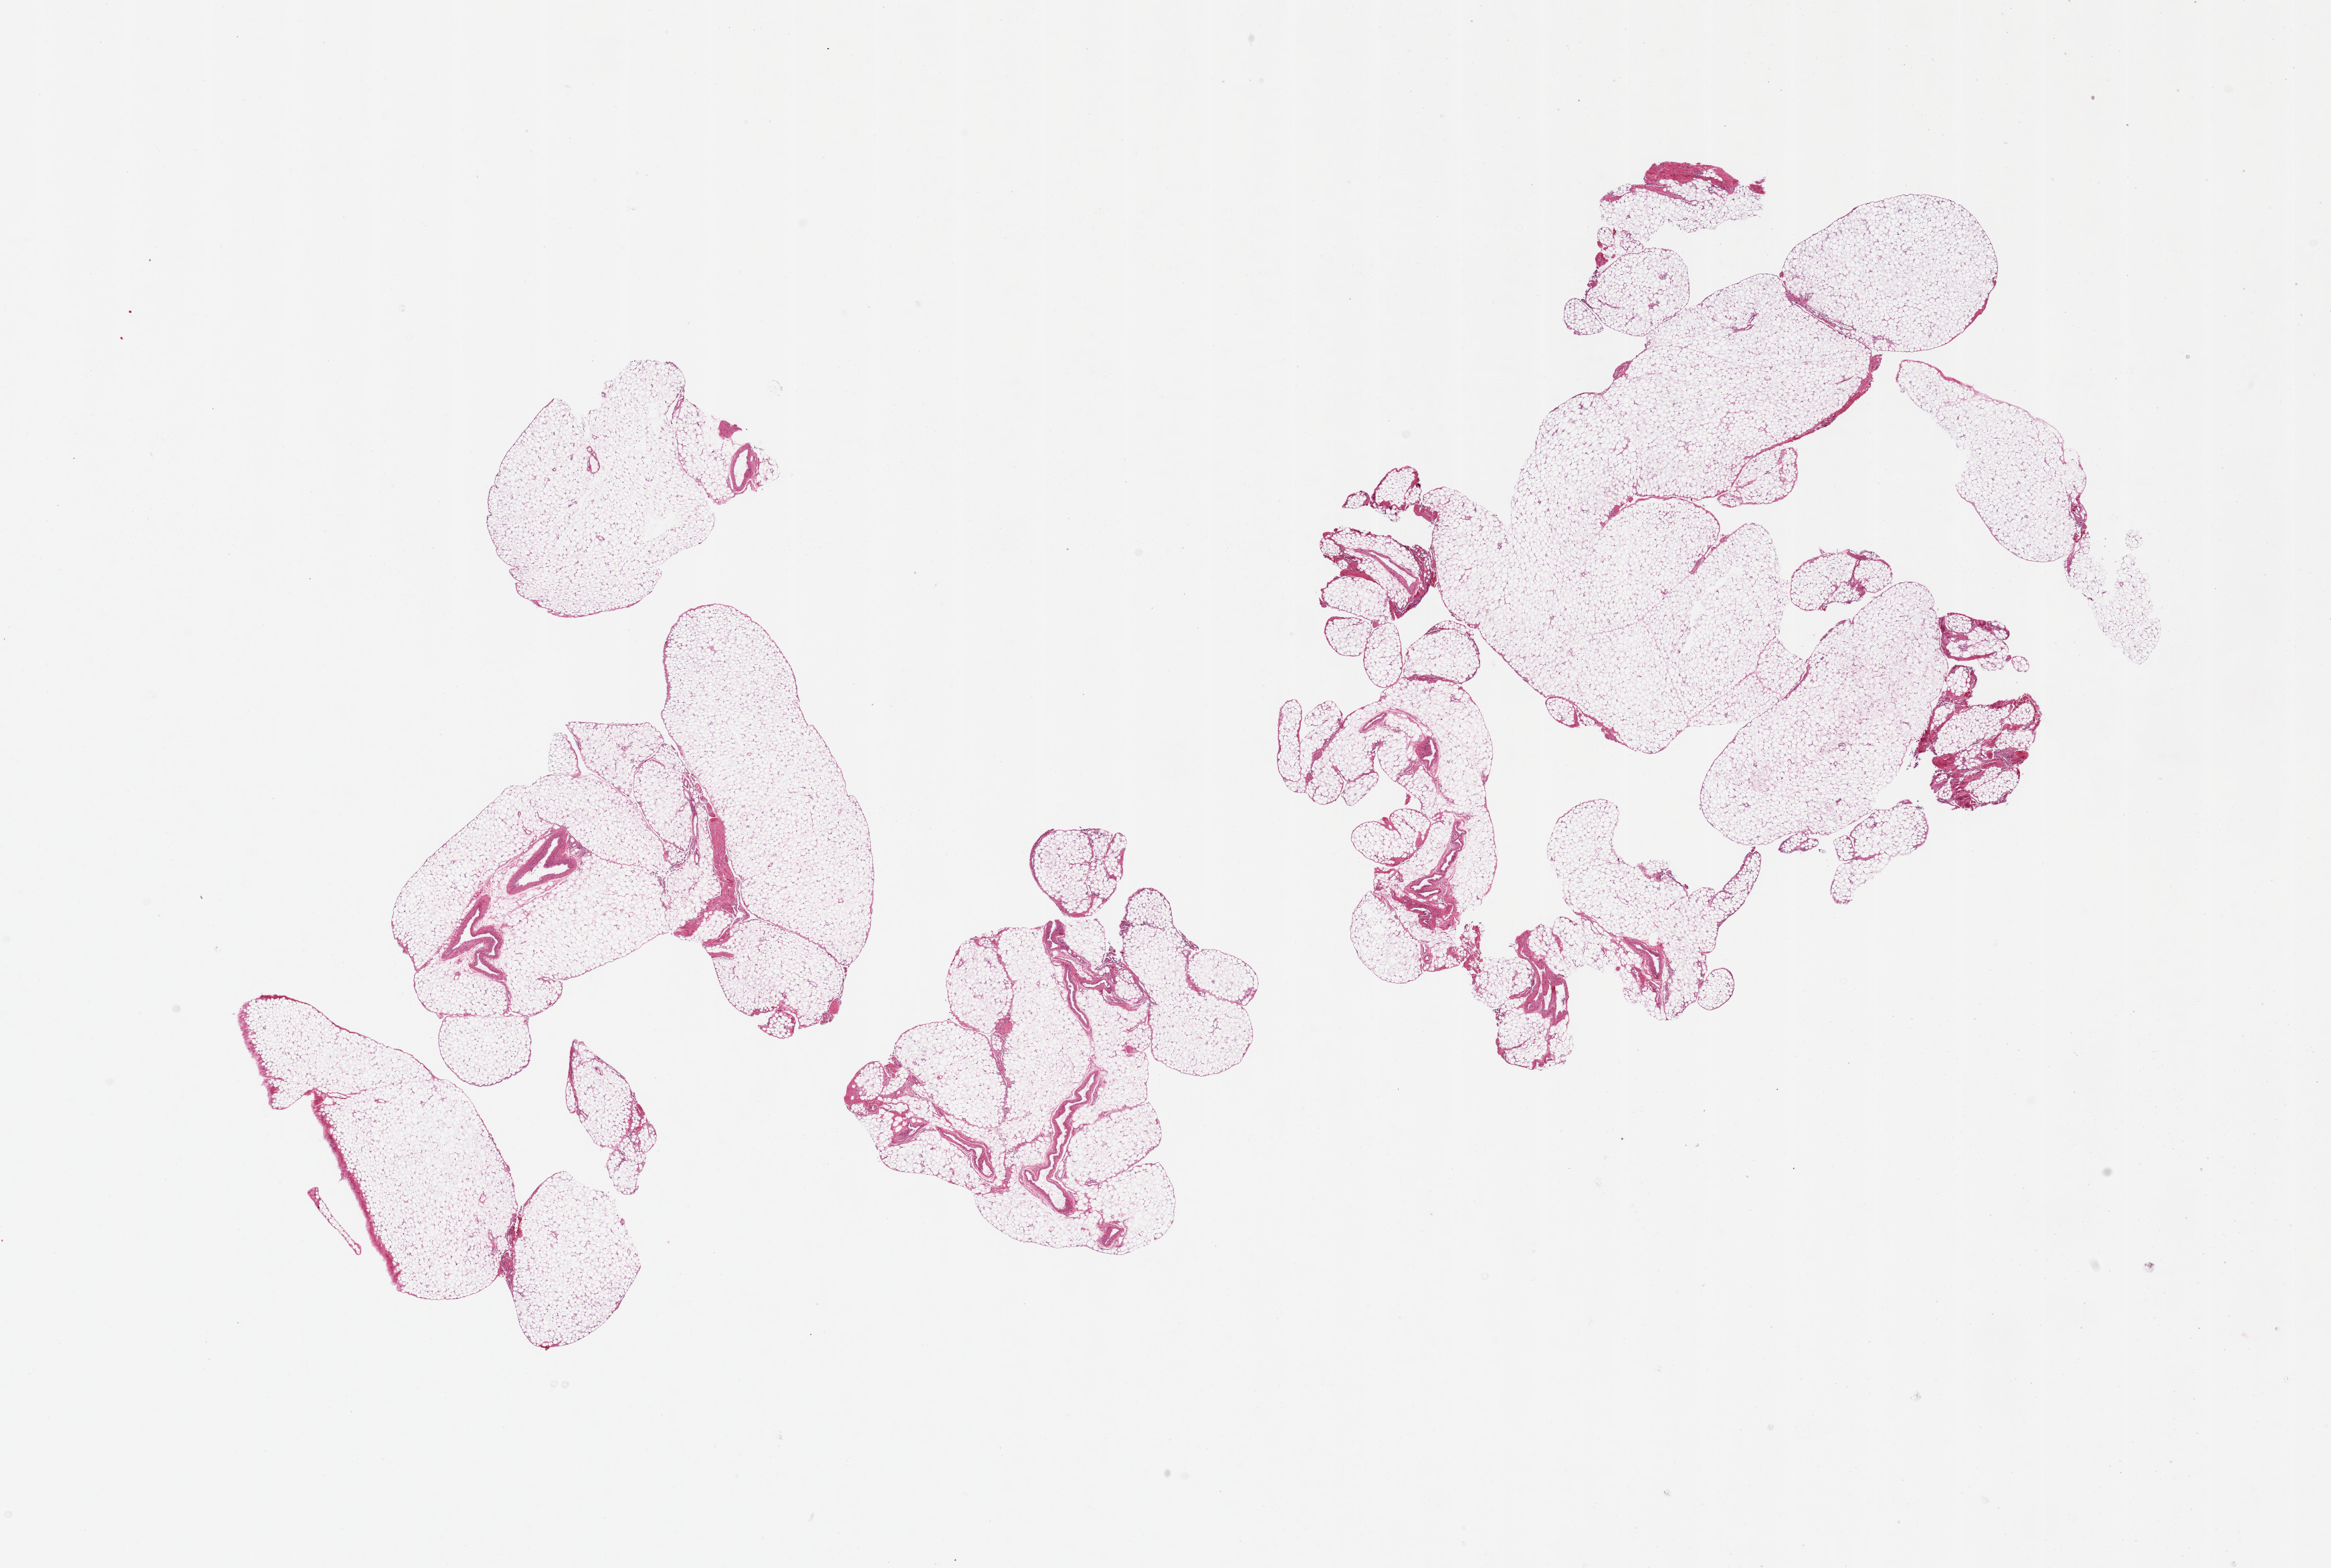
Digitized hematoxylin and eosin (H&E)-stained section — shown as a low-resolution overview of the whole scanned area (about 27.6 x 18.5 mm), PAXgene-fixed paraffin-embedded (PFPE) section, section of omentum (target tissue), donor tissue sample. Male donor.
Pathologist's review note for this sample: 2 pieces, ~10% vascular elements/mesothelial hyperplasia/fascia.